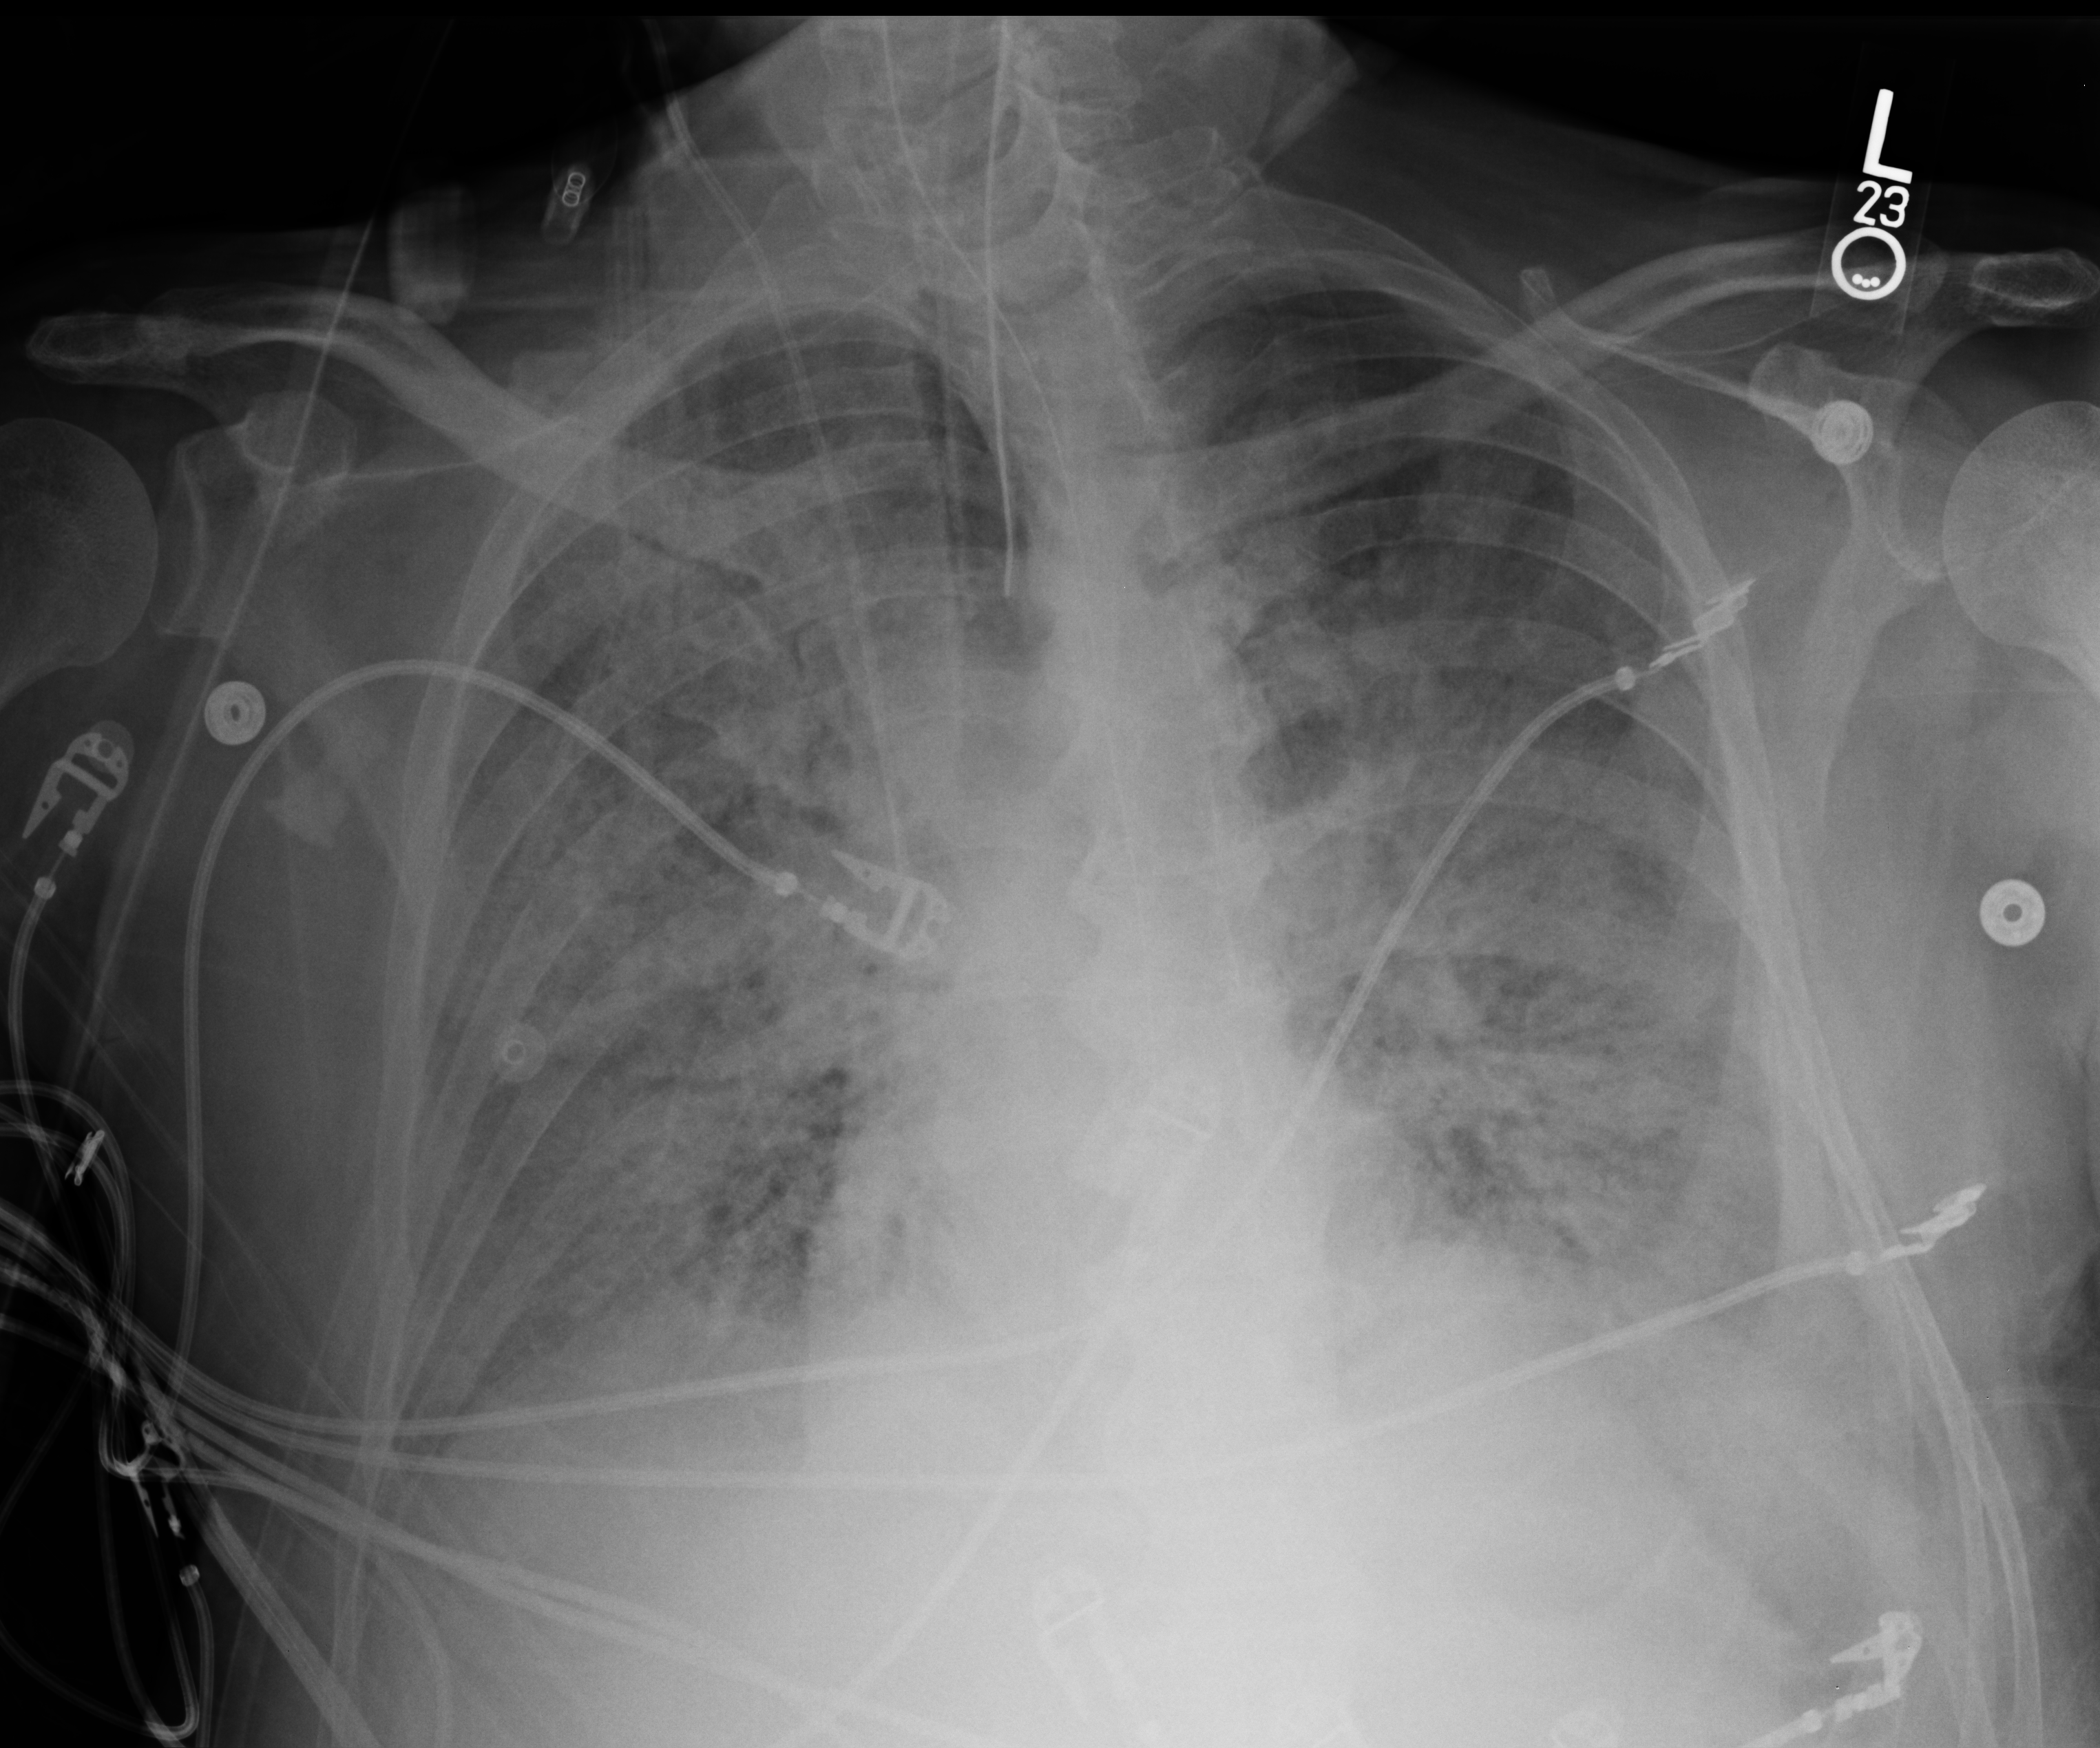
Portable chest radiograph. Patient hospitalised with COVID-19; male, aged 60–74 years.
From the hospital-stay record, not from the radiograph (when in the stay this image was taken is not recorded): admitted to intensive care during this hospital stay: yes.